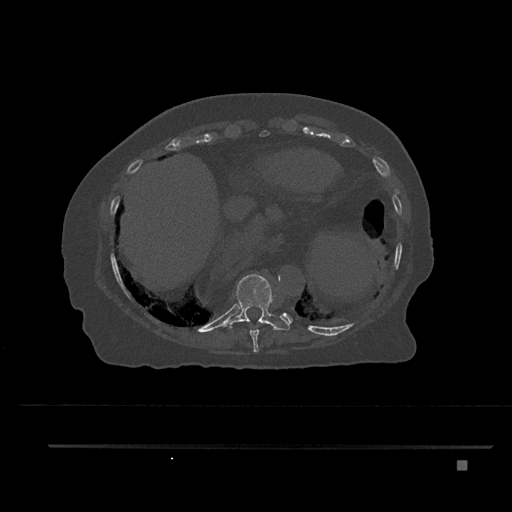
CT including the spine, one axial slice; position 369 of 797 along the scan axis; reconstruction kernel Br40s/3; 120 kVp; bone window (W 1800 / L 400 HU); 0.5 mm slice thickness; 512 × 512 image matrix, field of view 437 × 437 mm. Patient: female, 76 years. Case-level facts recorded for this patient, not image findings: primary cancer: lung.
Outlined on this slice (semi-automatically segmented with operator editing):
- T10 vertebra: box from (x=221, y=274) to (x=290, y=330) px
- T9 vertebra: (x=249, y=321)–(x=262, y=352)